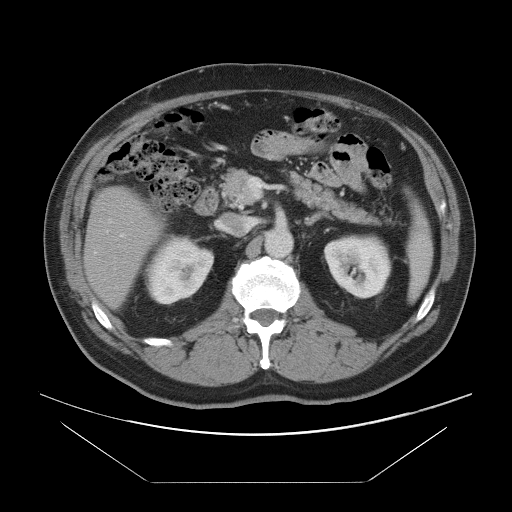
Contrast-enhanced abdominal CT, one axial slice; slice 44 of 97 in the series (ordered by position); intravenous contrast given; soft-tissue window (W 400 / L 40 HU); 5 mm slice thickness; 512 × 512 image matrix, field of view 442 × 442 mm. Male patient, age 62 years. Case-level facts recorded for this patient, not image findings: diagnosis: colorectal cancer liver metastases, imaged before liver resection; multiple liver metastases: no; largest metastasis: 7 cm; chemotherapy before resection: yes.
Annotated regions visible in this slice (expert manual segmentation):
- hepatic veins: bounding box <106,230,109,233> (left, top, right, bottom; pixels)
- liver: <85,188,161,306>
- planned liver remnant (the part of the liver to remain after resection): <85,187,162,306>
- portal vein (with intrahepatic branches): <120,234,124,237>